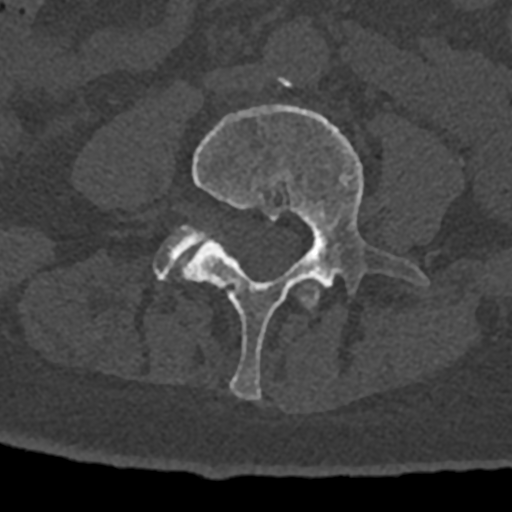
CT including the spine, one axial slice; position 255 of 797 along the scan axis; 120 kVp; bone window (W 1800 / L 400 HU); 0.5 mm slice thickness; 512 × 512 image matrix, field of view 160 × 160 mm. Male patient, age 74 years. Case-level facts recorded for this patient, not image findings: primary cancer: renal; vertebrae with lytic lesions (as recorded): T10, L1, L2, L3, L4, L5.
Annotated regions visible in this slice (semi-automatically segmented with operator editing):
- L3 vertebra: box from (x=299, y=277) to (x=320, y=309) px
- L4 vertebra: (x=182, y=105)–(x=429, y=400)
- L5 vertebra: (x=155, y=226)–(x=205, y=280)